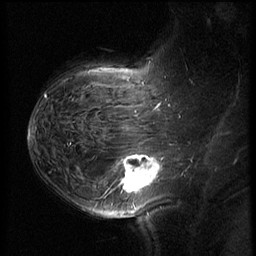
Breast MRI (dynamic contrast-enhanced), one sagittal slice. Position 44 of 62 along the scan axis. 3 images stored at this slice position (order not interpretable as contrast timing). 1.5 T. TE 4.2 ms, TR 8.9 ms. 2.5 mm slice thickness. 256 × 256 image matrix, field of view 200 × 200 mm. Patient: female, 37 years. From the clinical record (not read from this slice): setting: breast cancer imaged before/during neoadjuvant chemotherapy; receptor status: triple-negative.
Annotated regions visible in this slice (semi-automatic segmentation, software-assisted and operator-edited):
- analysis volume of interest (the breast-tissue region the enhancement analysis was run in; not a lesion): bounding box (x1, y1, x2, y2) in pixels: (116, 146, 168, 203)
- tumour enhancement mask (voxels above the 140 % enhancement threshold inside the analysis volume of interest): (121, 154, 161, 192)